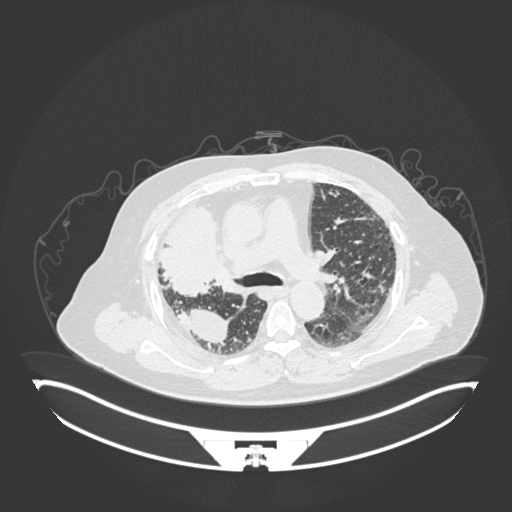
Chest CT, one axial slice; position 113 of 201 along the scan axis; lung window (W 1500 / L -600 HU); 1 mm slice thickness; 512 × 512 image matrix. Male patient, age 69 years. Case-level facts recorded for this patient, not image findings: clinical TNM (as recorded): T4 N3 M1.
Annotated regions visible in this slice (rectangle marked by the reading radiologist):
- lung tumour (recorded histology: adenocarcinoma): bounding box [x1, y1, x2, y2] px = [154, 201, 225, 296]